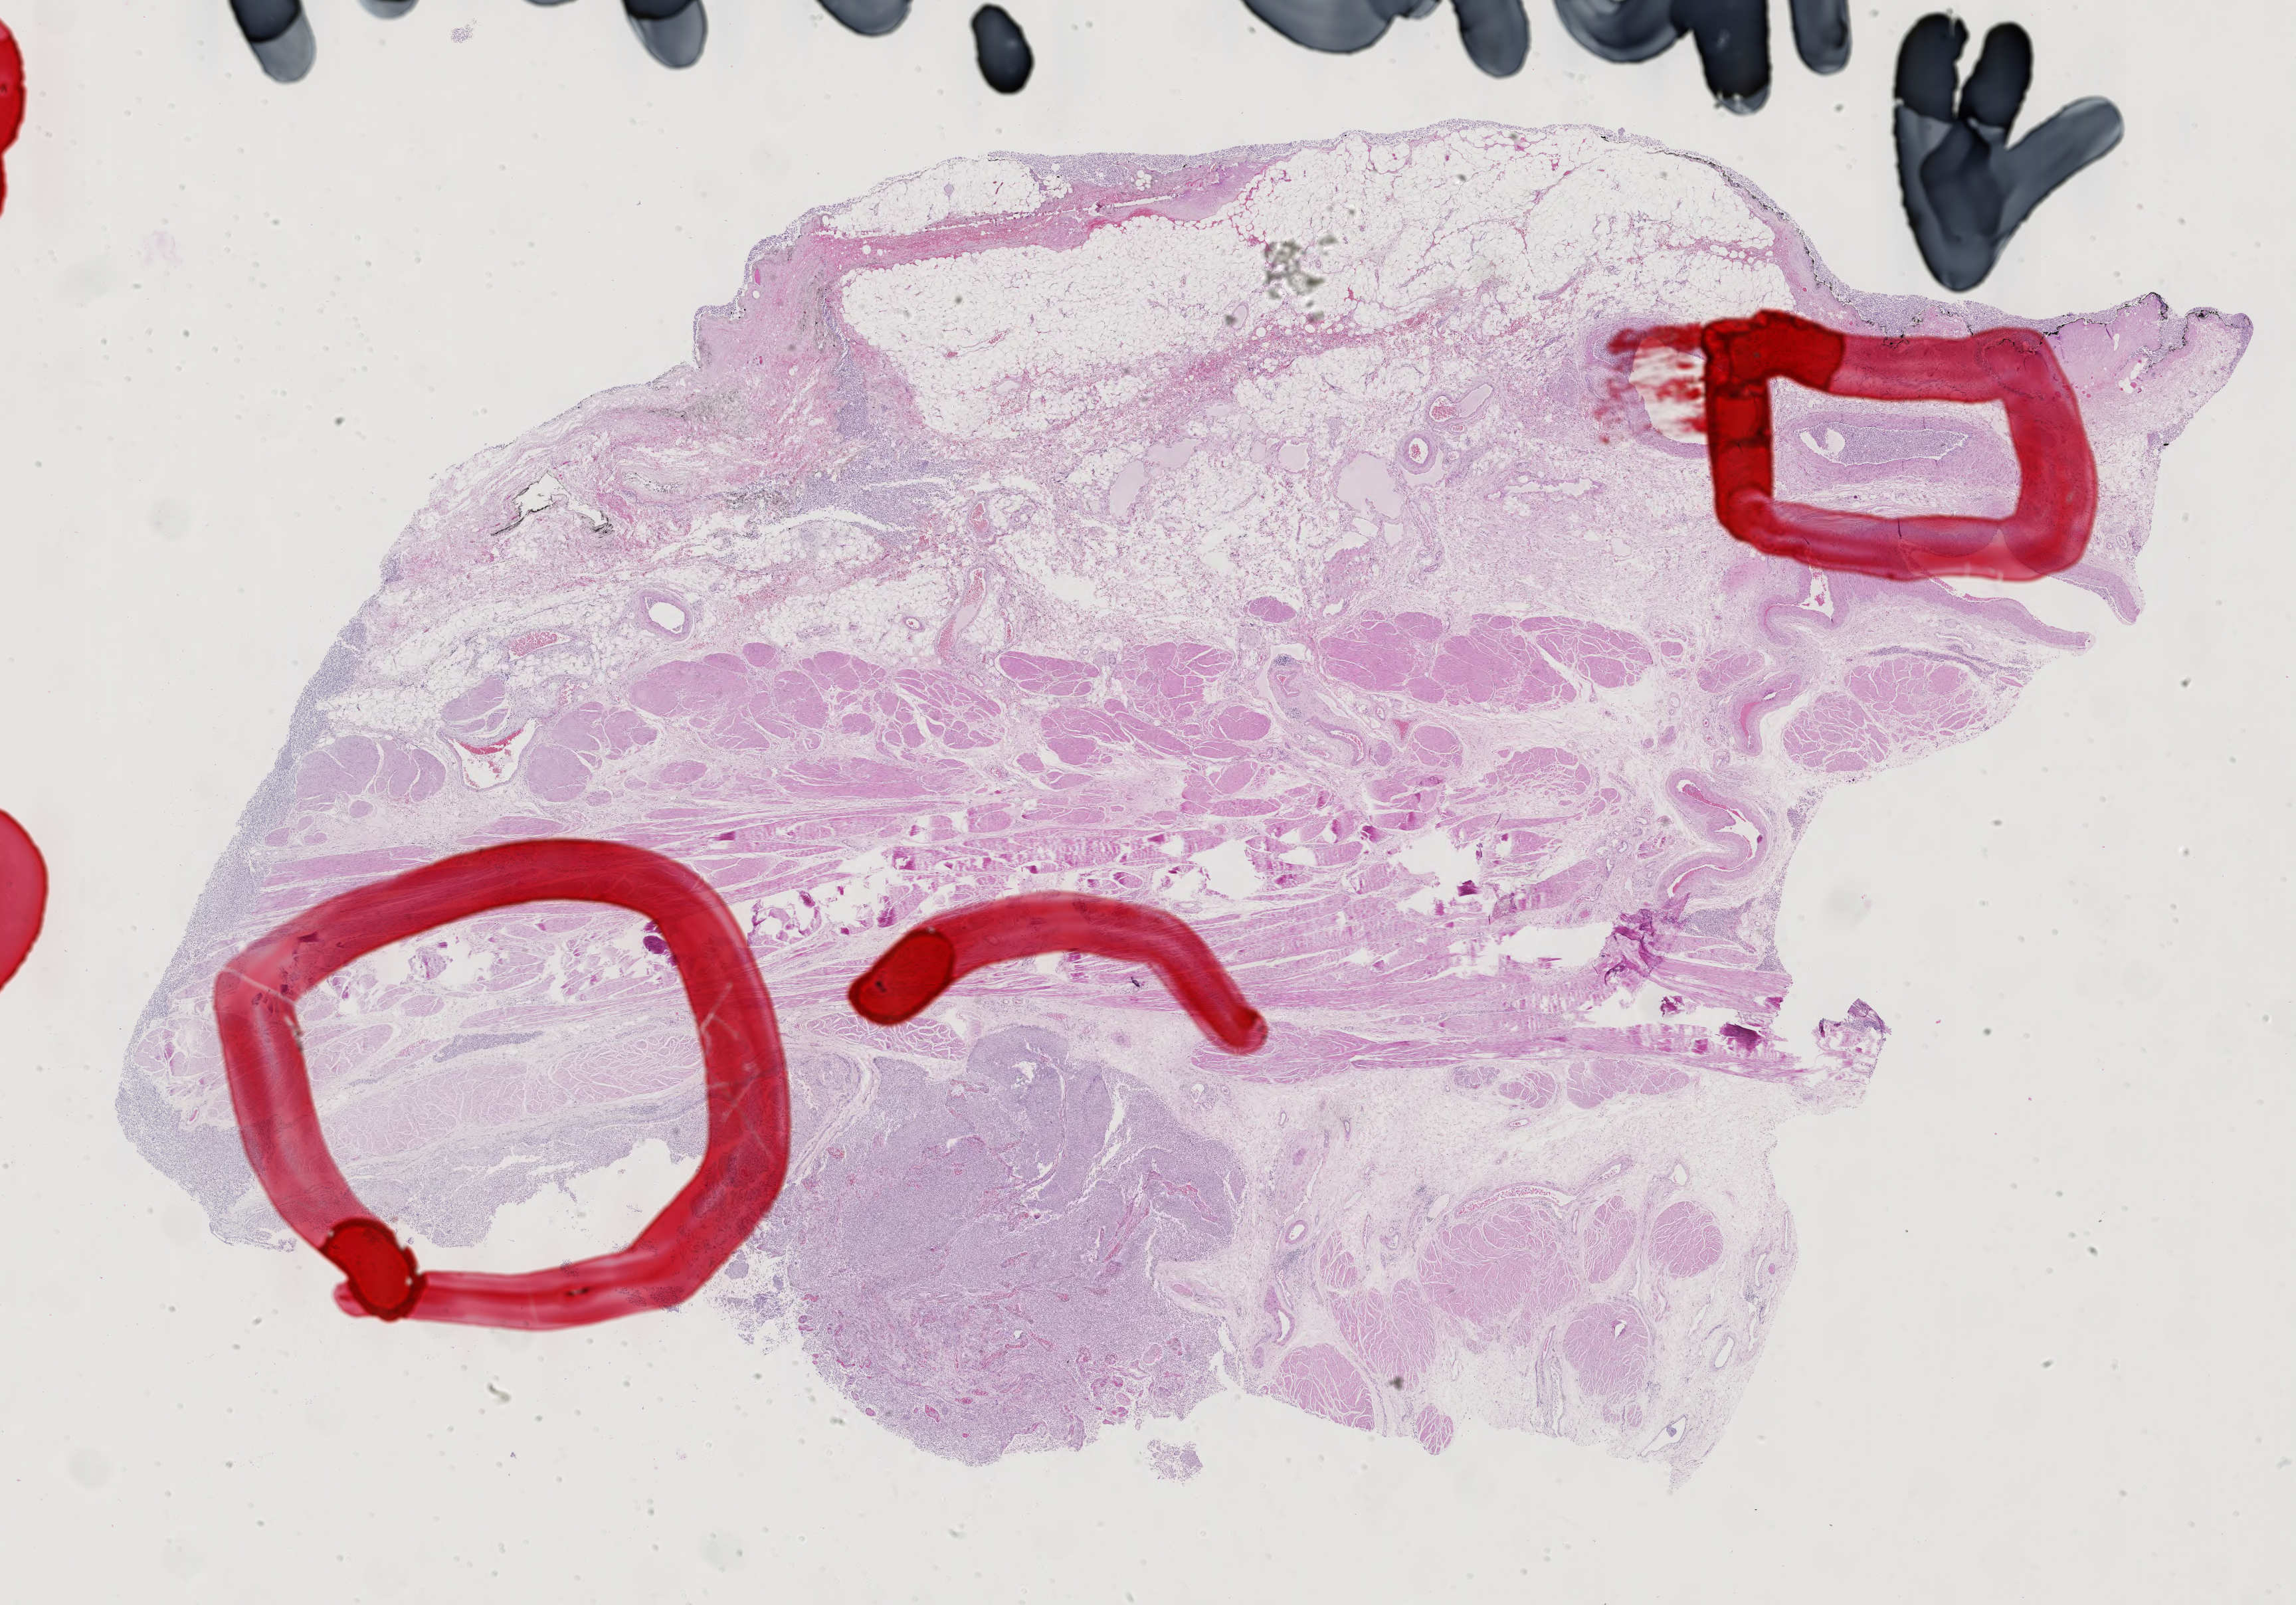
Whole-slide histology image, H&E, whole scanned area (about 25.2 x 17.6 mm, slide scanned at 40x) shown as a low-resolution overview, formalin-fixed paraffin-embedded (FFPE) diagnostic section, sample: primary tumour, bladder. Male patient; age at initial diagnosis 69 years.
Pathologic diagnosis: Transitional cell carcinoma.